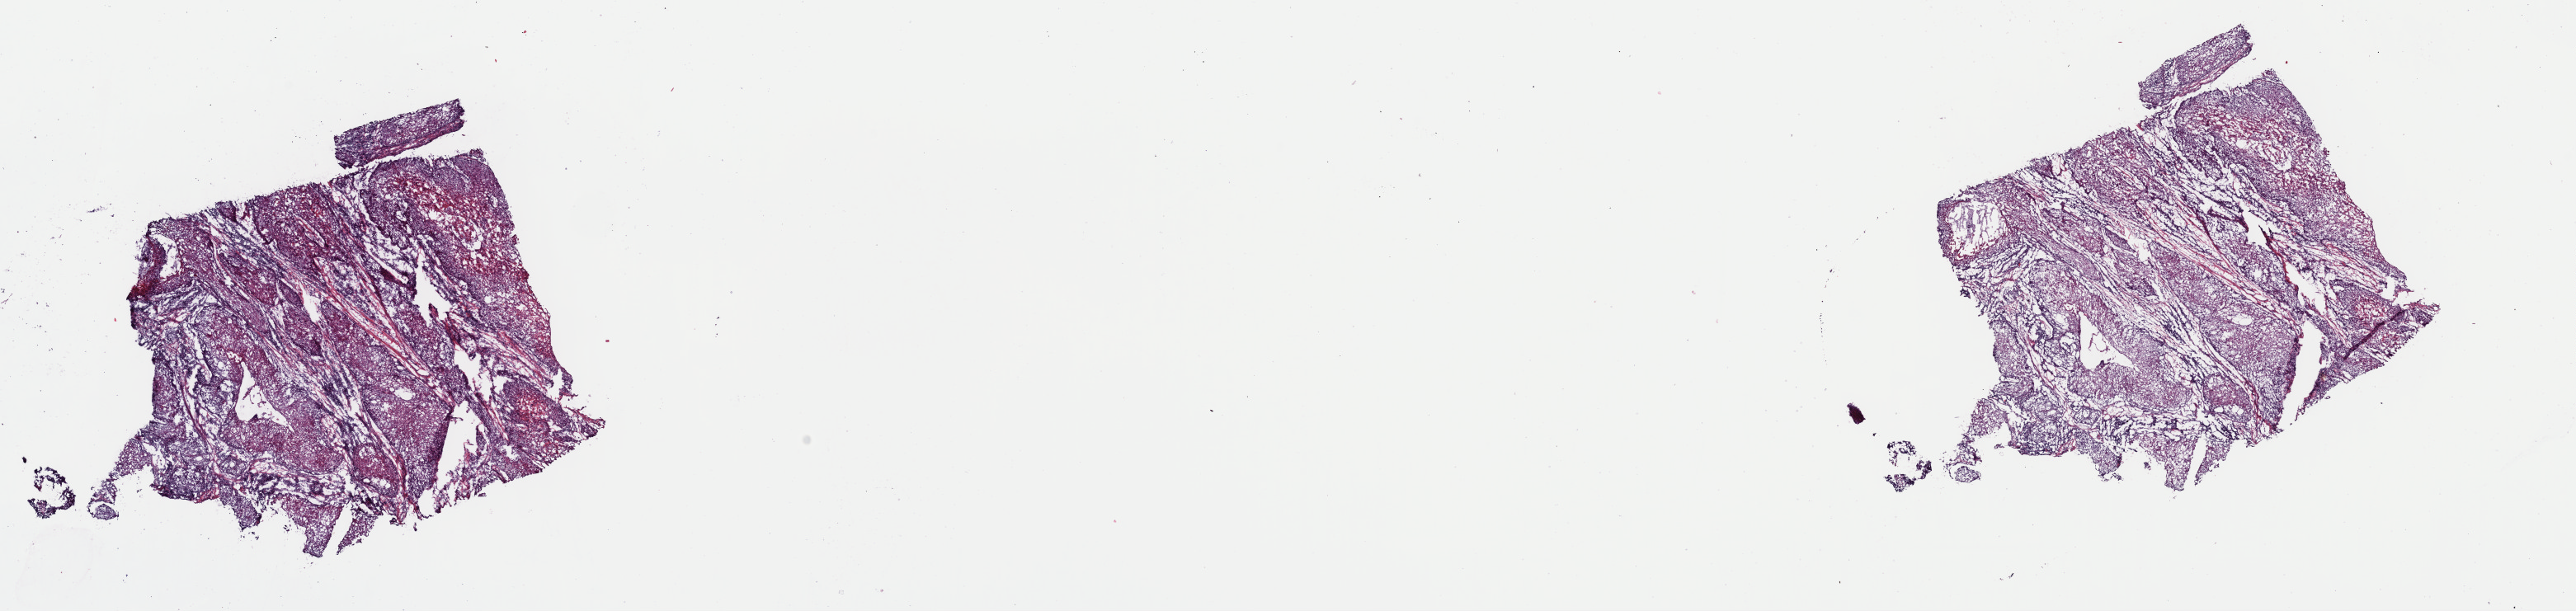
Hematoxylin and eosin (H&E) stained whole-slide image, shown as a low-resolution overview of the whole scanned area (about 24.7 x 5.9 mm, slide scanned at 40x). Frozen section from the top of the tissue portion. Primary tumour sample from the head and neck. Male, age 65 years at initial diagnosis. Histologic grade: G2 (moderately differentiated). Pathologist review of this section (percent, as recorded): tumour cells 90%, tumour nuclei 80%, normal cells 0%, stromal cells 0%, necrosis 10%. Inflammatory infiltration, as recorded: lymphocyte infiltration 4%, monocyte infiltration 0%, neutrophil infiltration 0%.
Diagnosis: Squamous cell carcinoma, NOS (larynx, NOS).